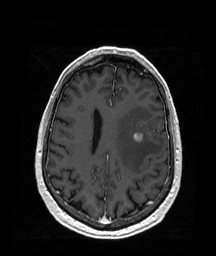
Brain MRI from a brain-tumour surgery series, one axial slice; slice 67 of 176 in the series (ordered by position); T1-weighted post-contrast; 1 mm slice thickness; 216 × 256 image matrix. Case-level facts recorded for this patient, not image findings: histopathology: Metastatic Melanoma; tumour location: Left Frontal.
Annotated regions visible in this slice (outlined manually by an expert reader):
- tumour: bounding box (x1, y1, x2, y2) in pixels: (133, 133, 144, 142)